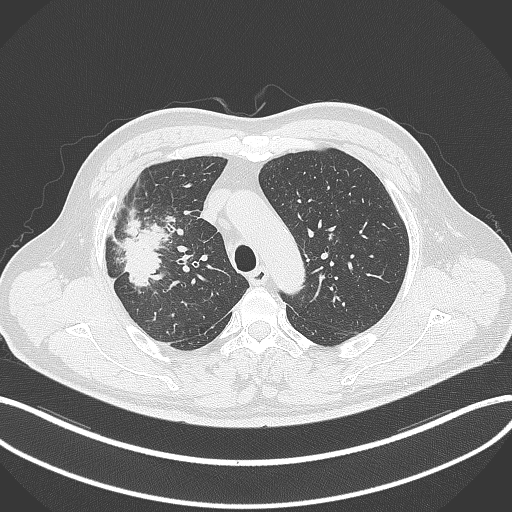
Chest CT, one axial slice; slice 253 of 348 in the series (ordered by position); reconstruction kernel B70f; lung window (W 1500 / L -600 HU); 1 mm slice thickness; 512 × 512 image matrix, field of view 400 × 400 mm. Male patient, age 55 years. Case-level facts recorded for this patient, not image findings: clinical TNM (as recorded): T3 N2 M1.
Outlined on this slice (rectangle marked by the reading radiologist):
- lung tumour (recorded histology: adenocarcinoma): bounding box (x1, y1, x2, y2) in pixels: (117, 215, 170, 291)